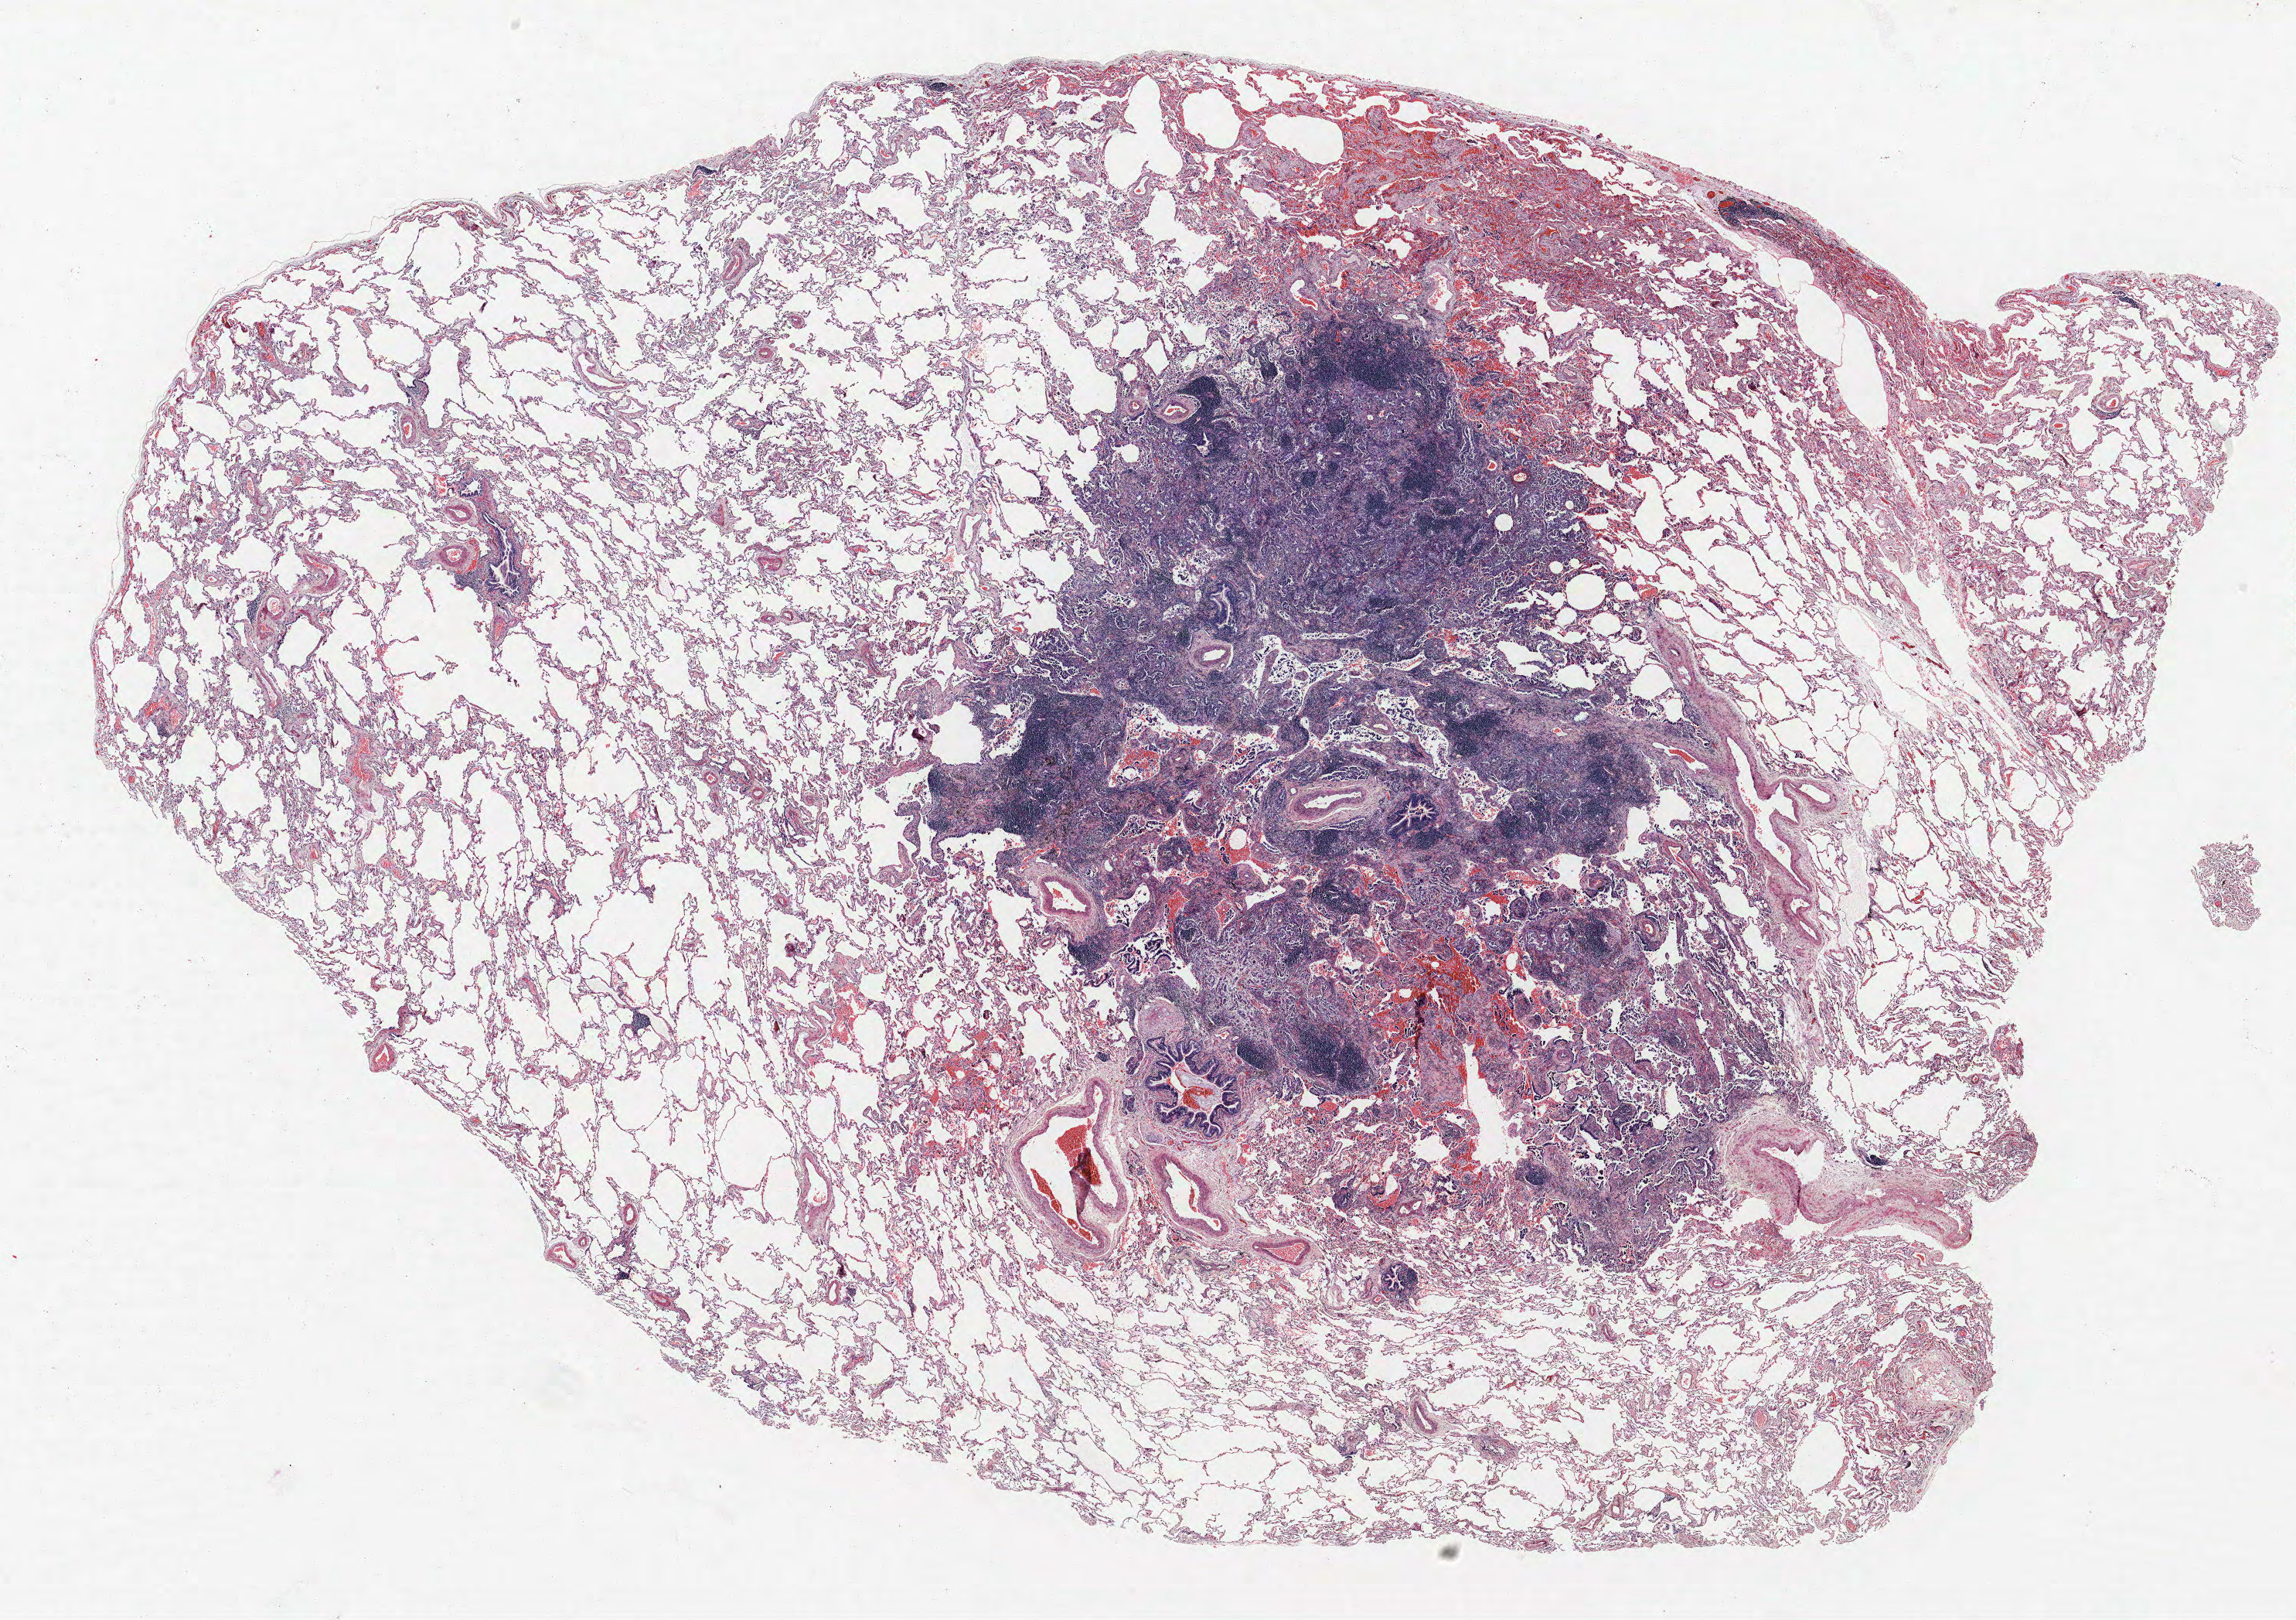
H&E-stained whole-slide image, whole scanned area (about 23.8 x 16.8 mm, acquisition: 40x scan) shown as a low-resolution overview, FFPE section, lung. Female, age 71 at enrolment. Current smoker at enrolment. Grade: moderately differentiated (G2).
Stage (AJCC 6th edition): IA. Participant's lung-cancer diagnosis: Adenocarcinoma, NOS. Tumour size (pathology): 12 mm. Primary tumour location (clinical record): right middle lobe.